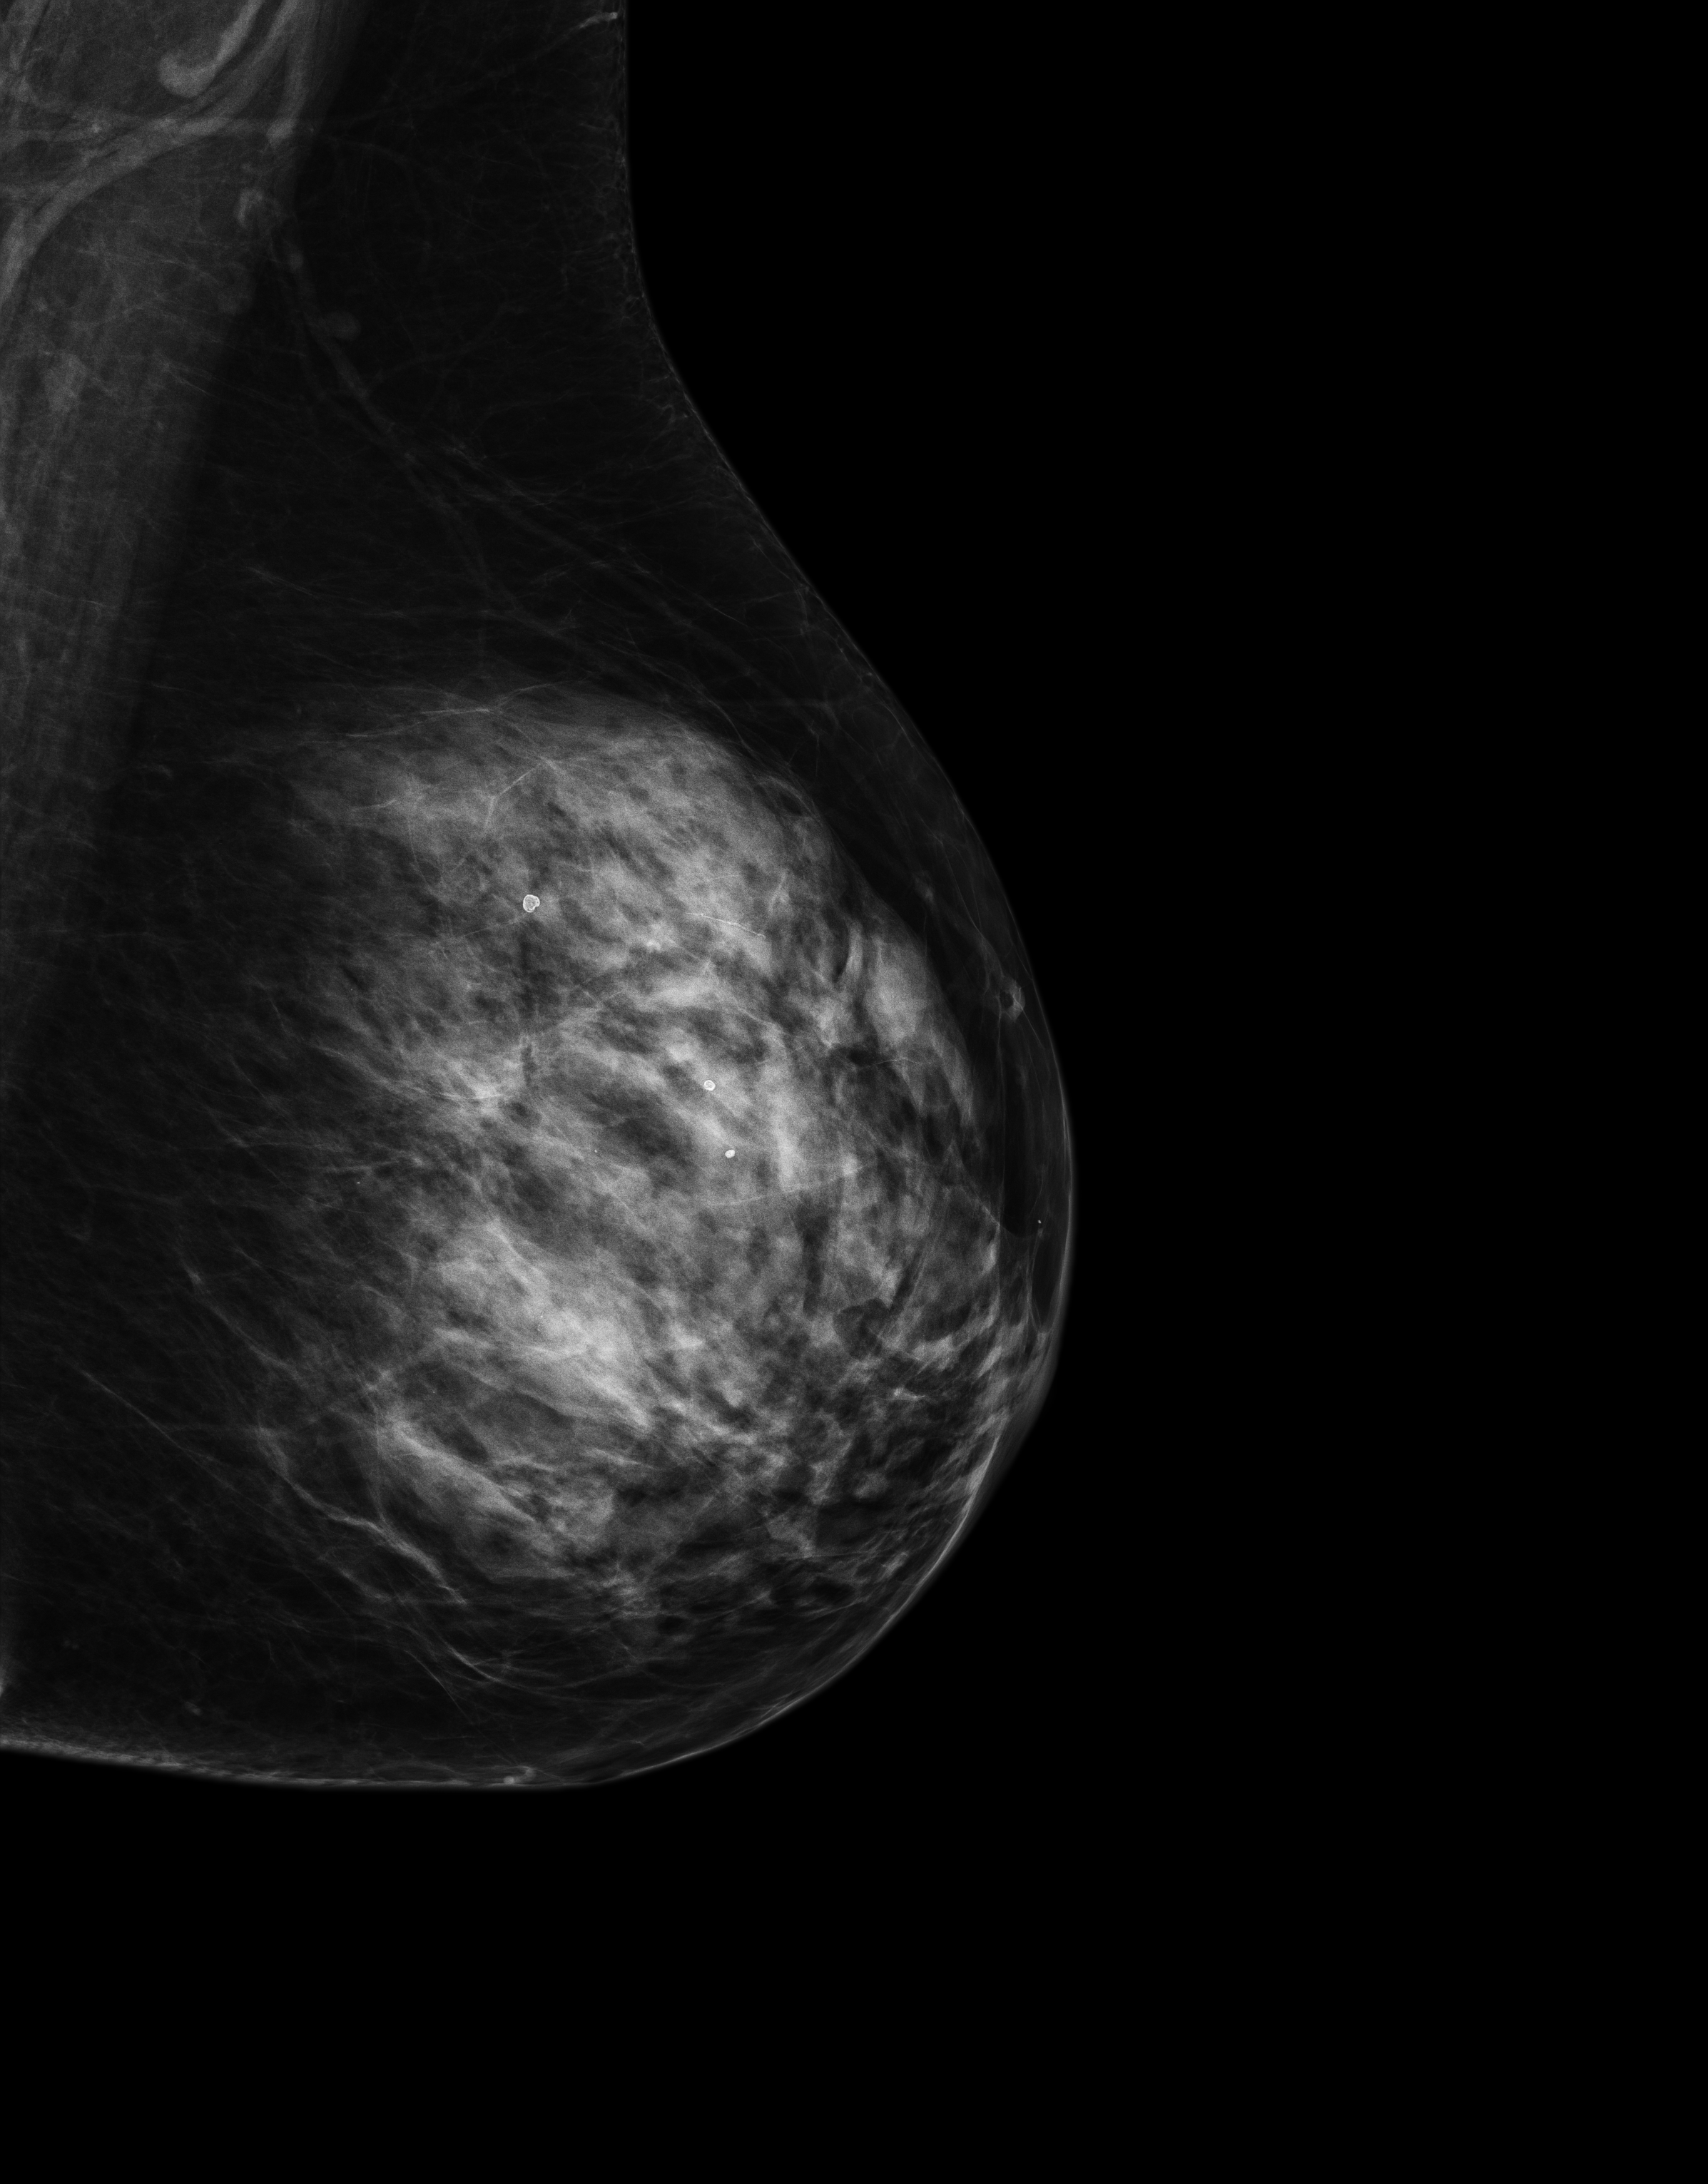
Digital mammogram (FFDM), left breast, MLO view, annual screening mammography examination, compressed breast thickness 55 mm, system: Senographe Essential ADS_56.21.3. Patient aged 65 years (female).
BI-RADS breast density category at the screening exam (both breasts, scale 1–4): 3. Final BI-RADS category for the screening round (tomosynthesis exam, both breasts): category 1. Recall: no recall after this screen.